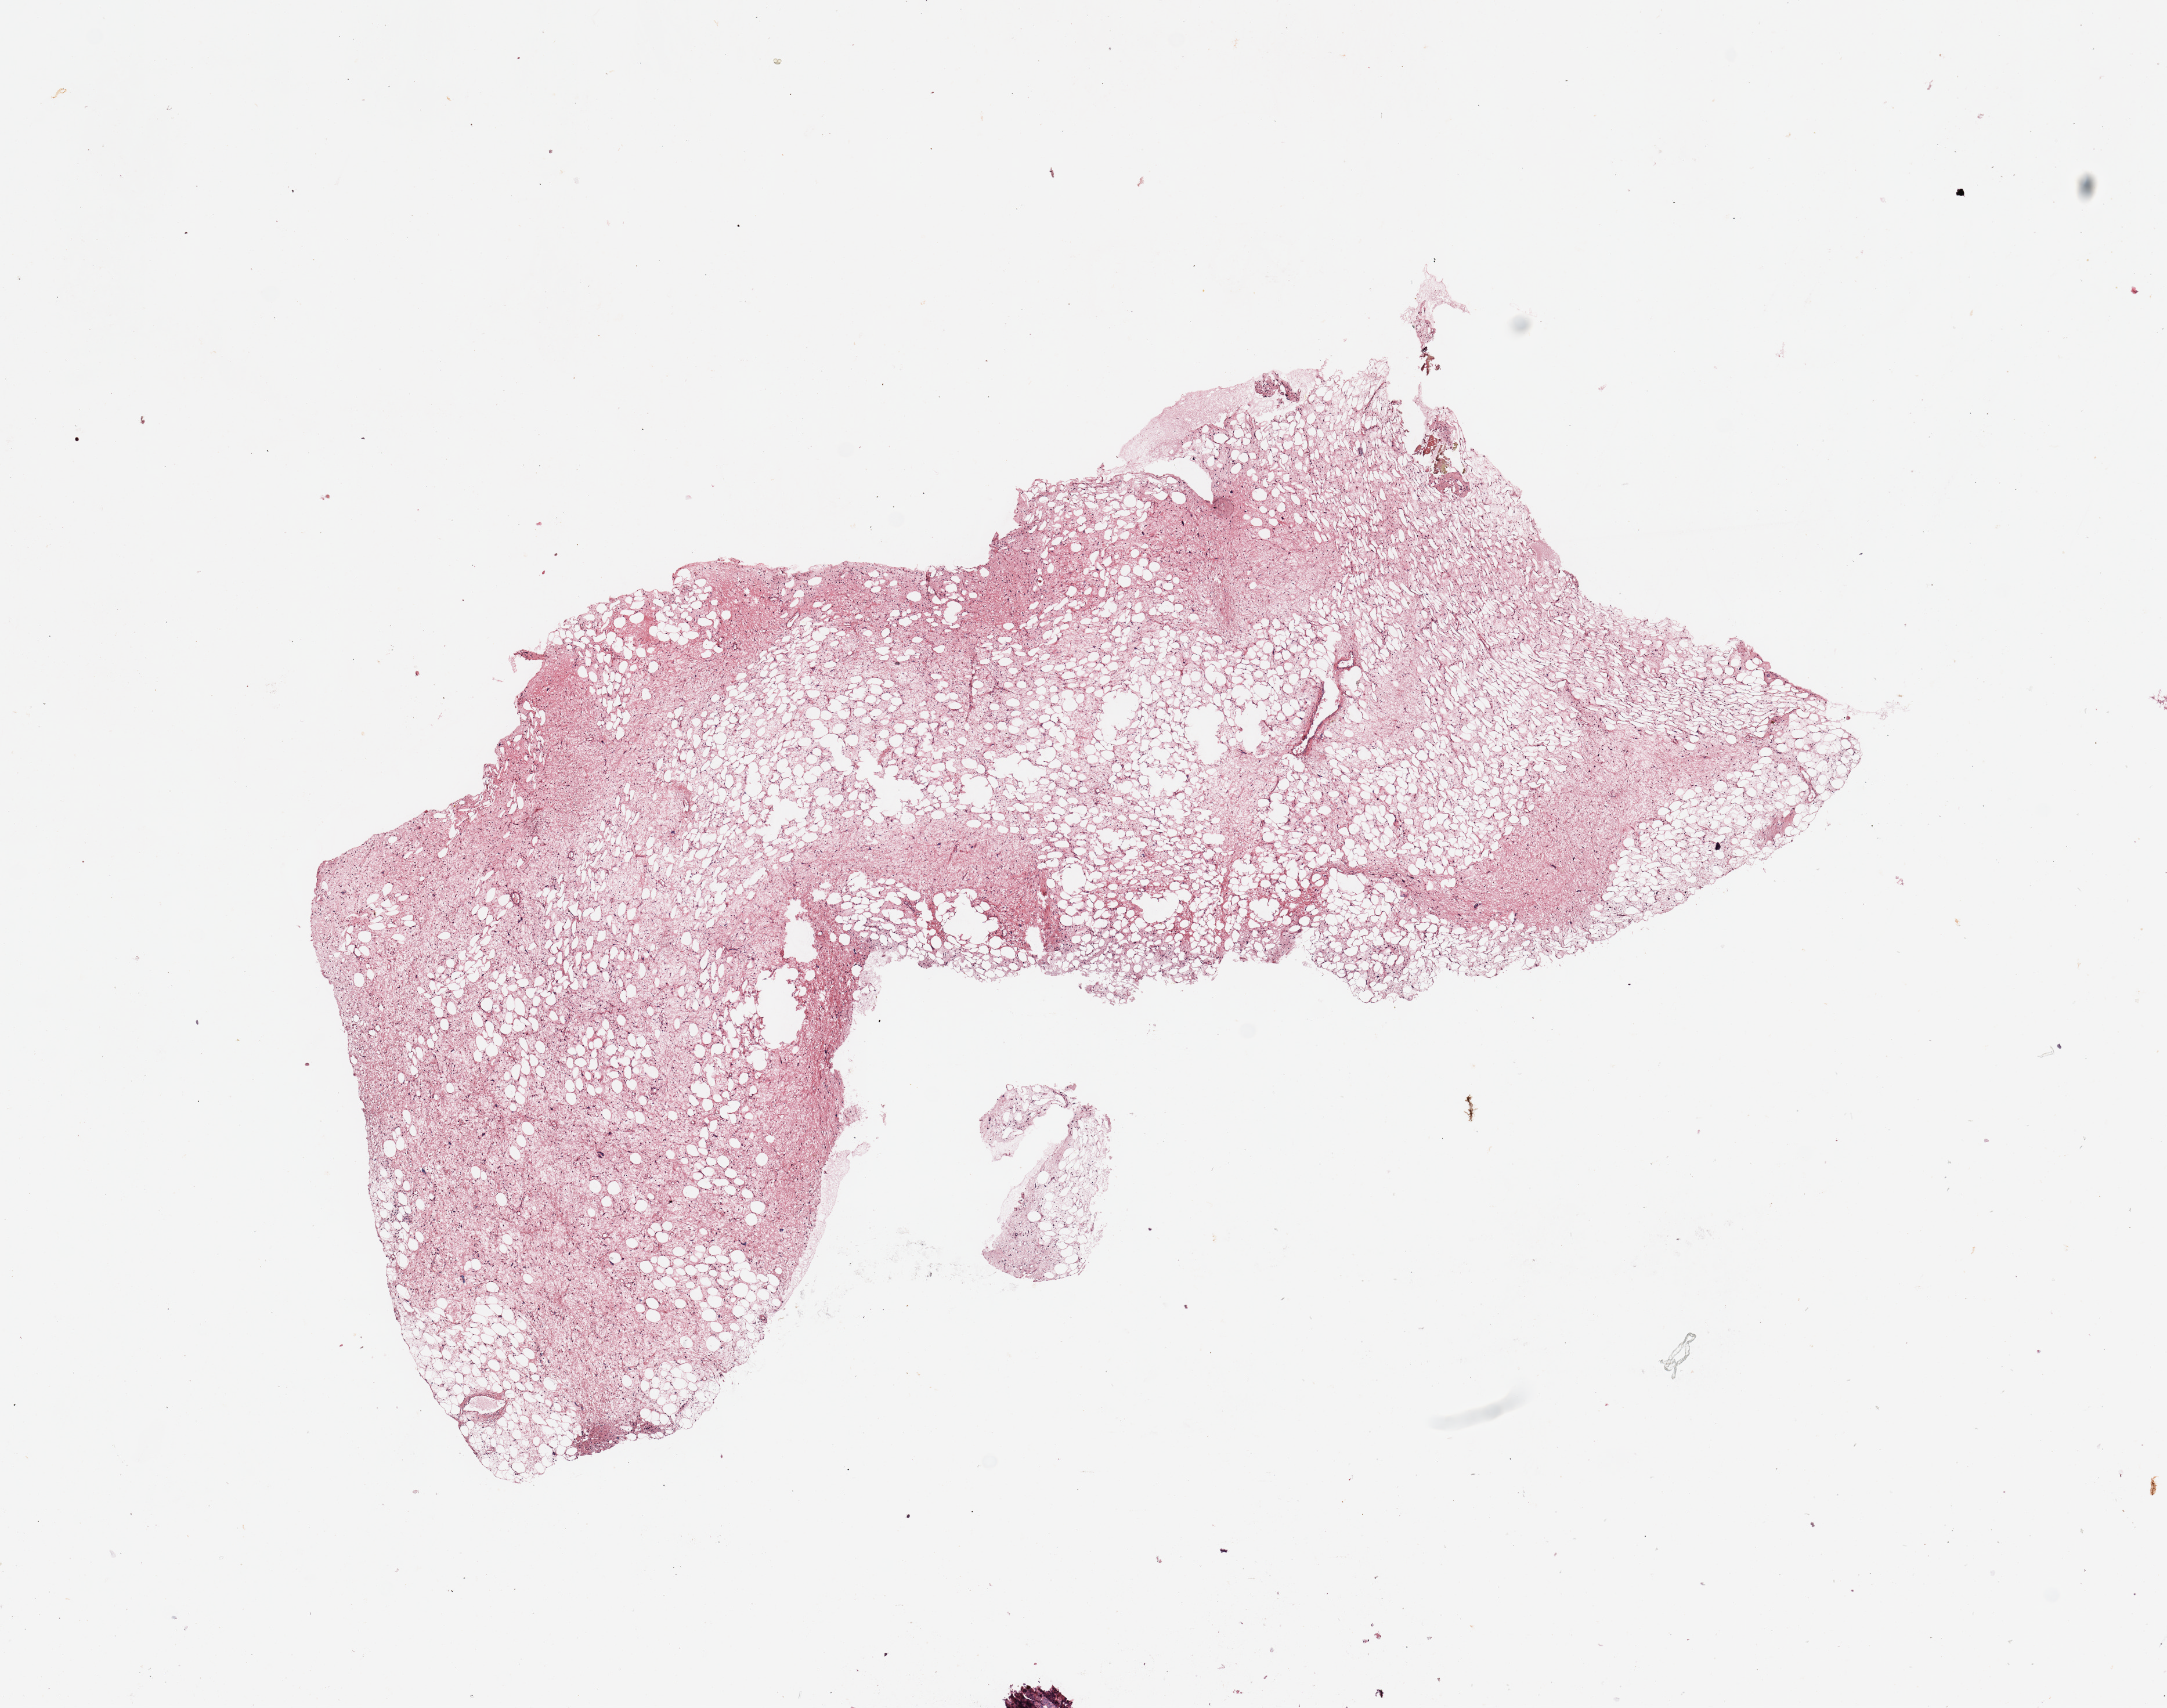
Hematoxylin and eosin (H&E) stained whole-slide image — shown as a low-resolution overview of the whole scanned area (about 14.8 x 11.6 mm, slide scanned at 20x), tumour tissue sample. Female, 65 y/o.
Patient diagnosis (cohort enrolment): sarcoma (site not recorded at cohort level).